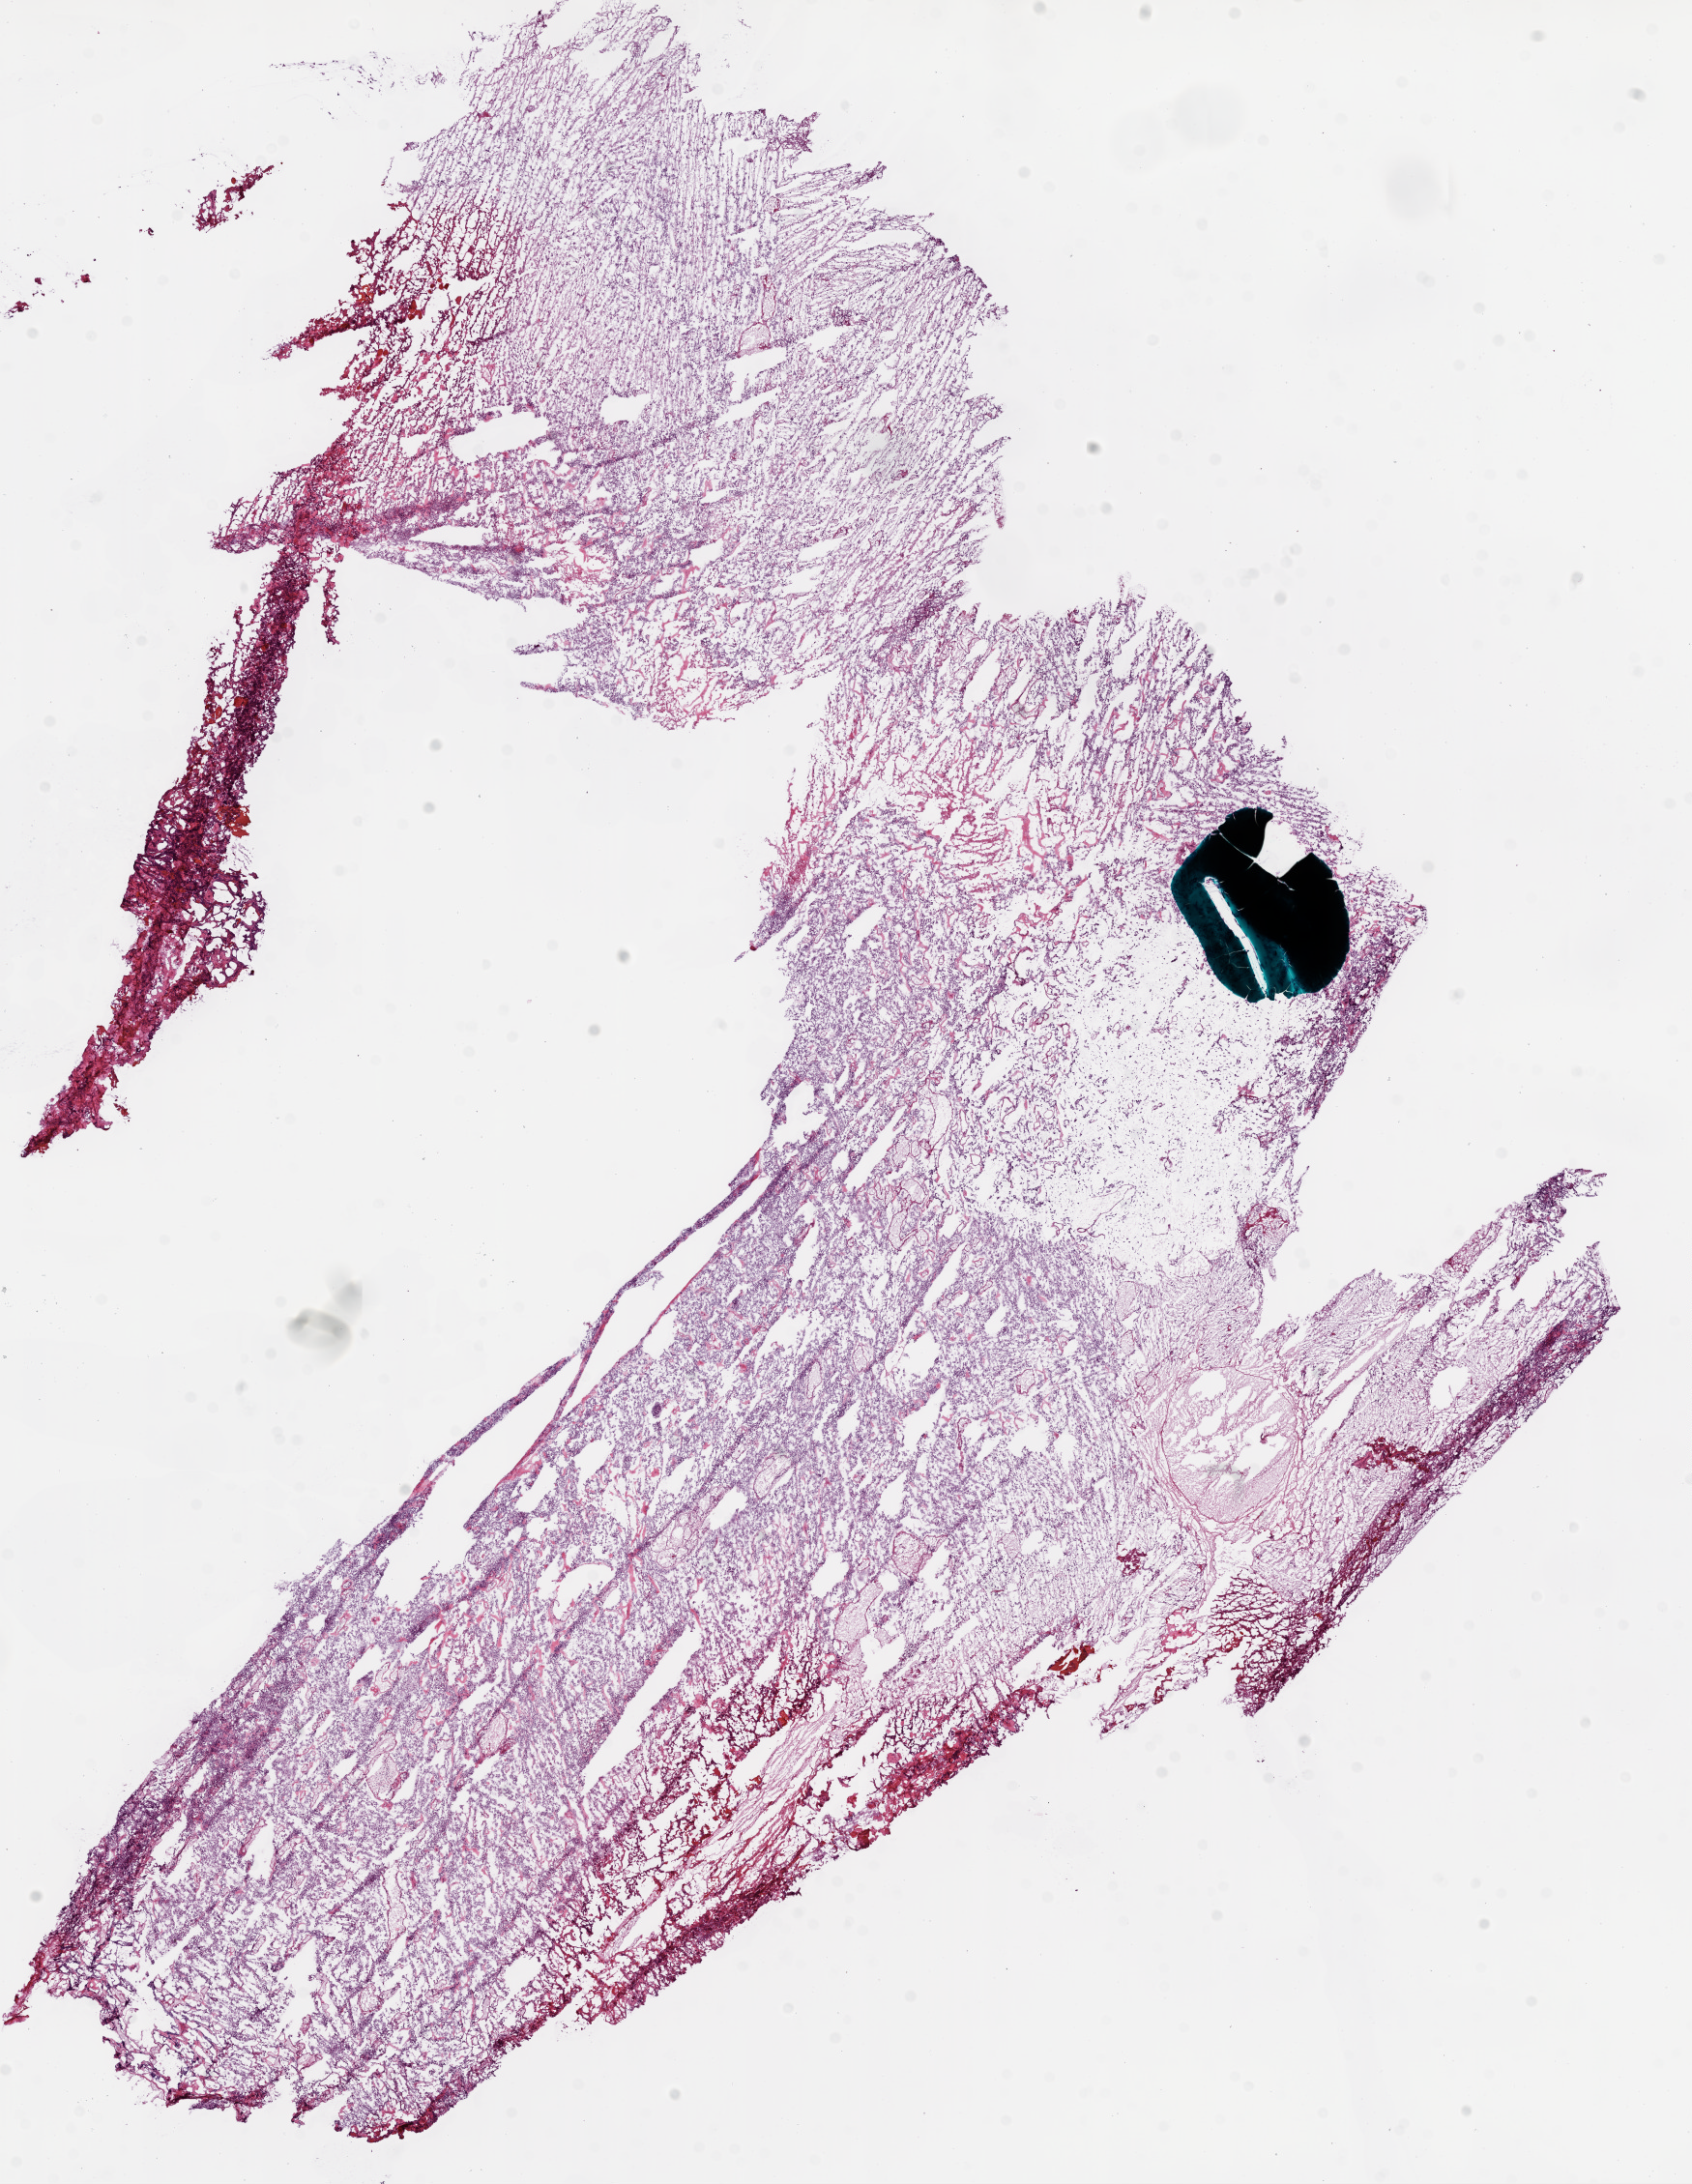
Digitized Hematoxylin and eosin (H&E) stained tissue section (whole slide) — low-resolution overview of the scanned area, about 14.0 x 18.1 mm (acquisition: 20x scan); frozen section from the bottom of the tissue portion; sample: primary tumour, brain. Patient: female, age at initial diagnosis 36 years. Slide review estimates, as recorded: tumour cells 95%, tumour nuclei 100%, normal cells 0%, stromal cells 0%, necrosis 5%.
Histologic diagnosis: Glioblastoma.